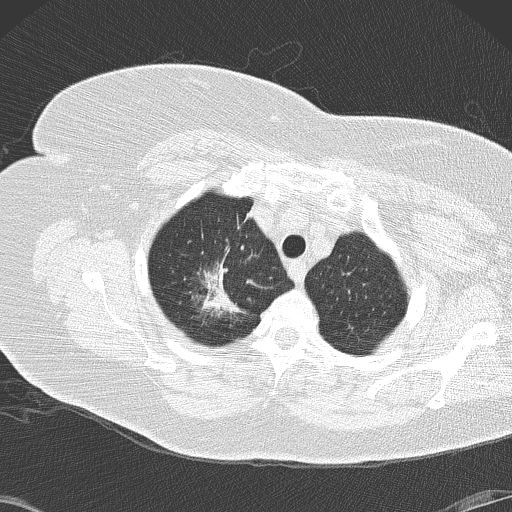
Axial slice from a low-dose chest CT screening exam, second annual screen, lung window (W 1500 / L -600 HU), 2 mm slice thickness, slice 23 of 146 in the series. Female, age 72 years at enrolment. Former smoker at enrolment.
Lesion marked by an expert reader, box from (x=181, y=244) to (x=260, y=327) px. The screening reader recorded 4 non-calcified nodules or masses ≥4 mm on this exam; which of them this box marks is not recorded. Later outcome: lung cancer diagnosed 52 days after this screen — bronchiolo-alveolar adenocarcinoma, NOS, right upper lobe, stage IIIB (AJCC 6th edition), 45 mm at pathology.